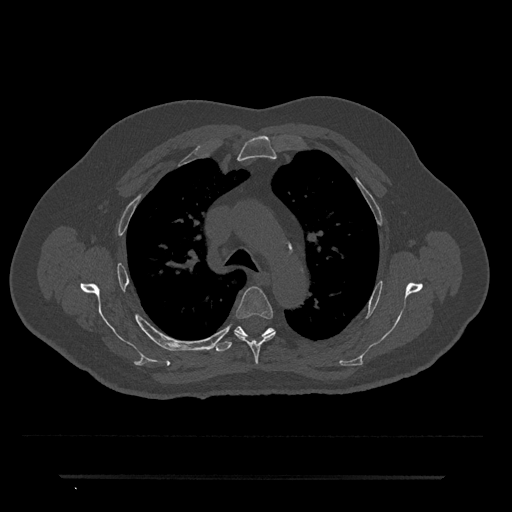
CT including the spine, one axial slice. Position 513 of 797 along the scan axis. Reconstruction kernel Br40s/3. 120 kVp. Bone window (W 1800 / L 400 HU). 0.5 mm slice thickness. 512 × 512 image matrix. Male patient, age 69 years. From the clinical record (not read from this slice): primary cancer: prostate.
Annotated regions visible in this slice (semi-automatically segmented with operator editing):
- T4 vertebra: box from (x=234, y=287) to (x=275, y=364) px
- T5 vertebra: (x=213, y=326)–(x=274, y=352)